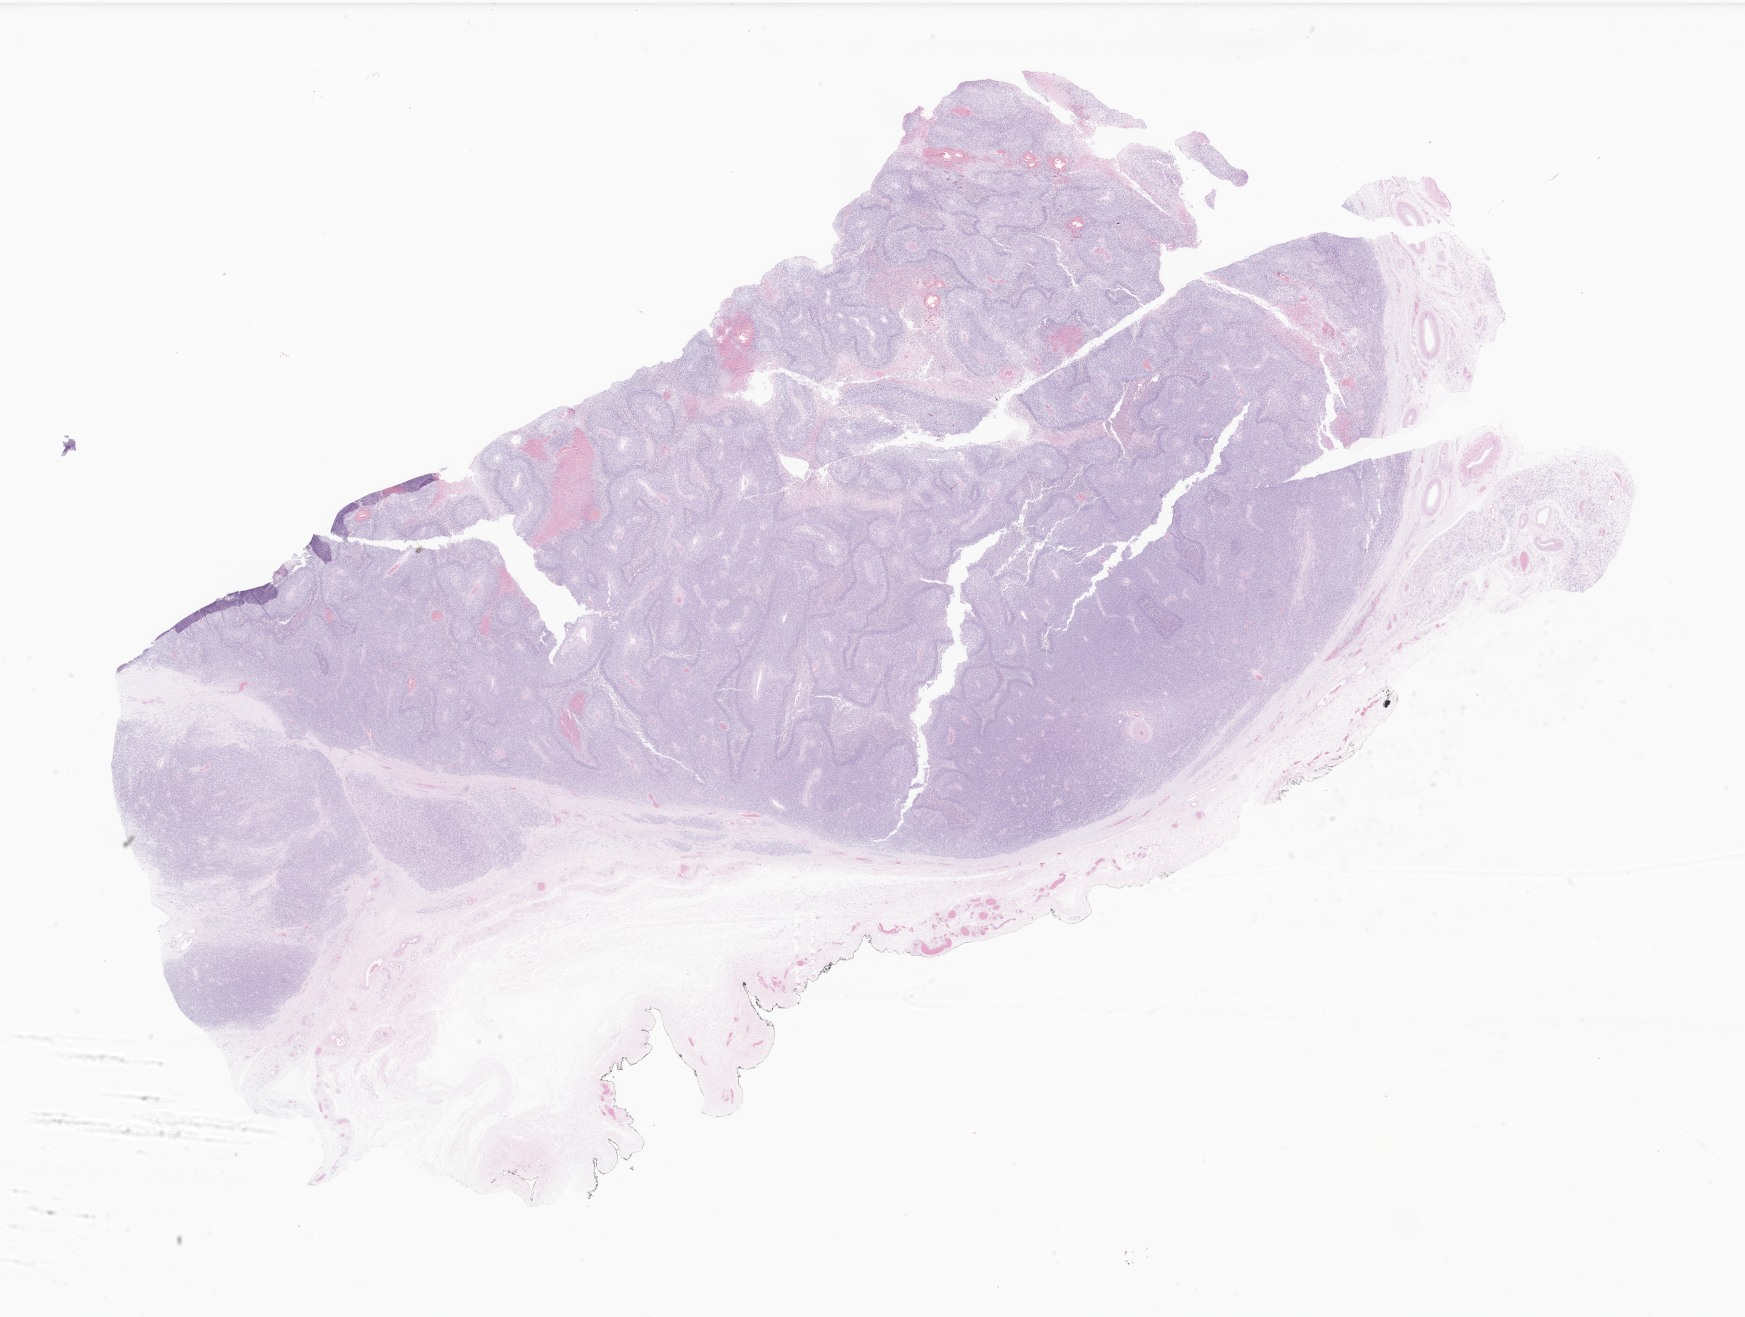
Digitized haematoxylin and eosin-stained section of tumor tissue from the testis — shown as a low-resolution overview of the whole scanned area (about 29.4 x 22.2 mm), FFPE section. Patient male; age 212 months (17 years 8 months).
Diagnosis: Embryonal rhabdomyosarcoma, NOS.